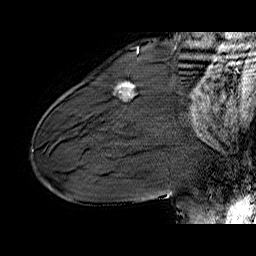
Breast MRI (dynamic contrast-enhanced), one sagittal slice; position 20 of 60 along the scan axis; dynamic contrast-enhanced series, time point 2 of 6 at this slice position (early post-contrast); 1.5 T; TE 6.4 ms, TR 32.9 ms; 4 mm slice thickness; 256 × 256 image matrix, field of view 200 × 200 mm. Female patient. Case-level facts recorded for this patient, not image findings: setting: breast cancer imaged before/during neoadjuvant chemotherapy; receptor status: HER2-positive.
Structures marked on this image (semi-automatically segmented with operator editing):
- analysis volume of interest (the breast-tissue region the enhancement analysis was run in; not a lesion): bounding box (x1, y1, x2, y2) in pixels: (115, 82, 135, 102)
- tumour enhancement mask (voxels above the 100 % enhancement threshold inside the analysis volume of interest): (123, 85, 134, 88)